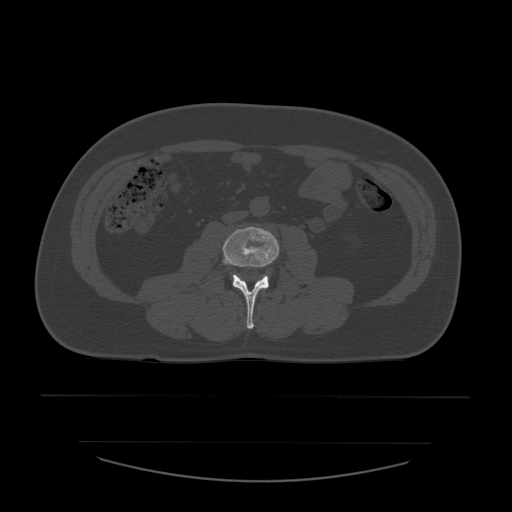
CT including the spine, one axial slice. Slice 168 of 532 in the series (ordered by position). Reconstruction kernel STANDARD. Bone window (W 1800 / L 400 HU). 1.25 mm slice thickness. 512 × 512 image matrix. Patient age 44 years. From the clinical record (not read from this slice): primary cancer: soft tissue sarcoma.
Annotated regions visible in this slice (semi-automatically segmented with operator editing):
- L3 vertebra: box from (x=223, y=227) to (x=280, y=329) px